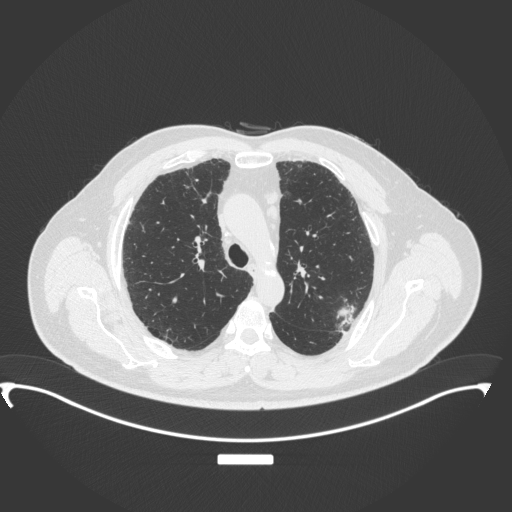
Chest CT, one axial slice; position 256 of 350 along the scan axis; reconstruction kernel B31f; lung window (W 1500 / L -600 HU); 1 mm slice thickness; 512 × 512 image matrix. Patient: male, 64 years. From the clinical record (not read from this slice): clinical TNM (as recorded): T1c N1 M1.
Structures marked on this image (rectangle marked by the reading radiologist):
- lung tumour (recorded histology: adenocarcinoma): bounding box <335,301,363,333> (left, top, right, bottom; pixels)